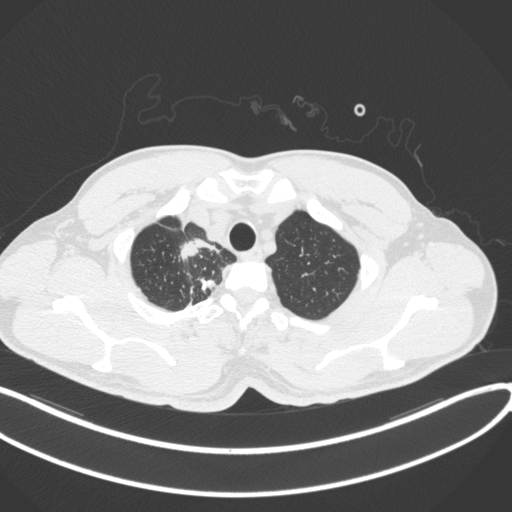
Chest CT, one axial slice; position 333 of 391 along the scan axis; 120 kVp; lung window (W 1500 / L -600 HU); 512 × 512 image matrix, field of view 400 × 400 mm. Patient: male, 48 years. From the clinical record (not read from this slice): clinical TNM (as recorded): T1c N1 M1.
Structures marked on this image (bounding box drawn by a radiologist):
- lung tumour (recorded histology: adenocarcinoma): bounding box [x1, y1, x2, y2] px = [177, 232, 223, 267]